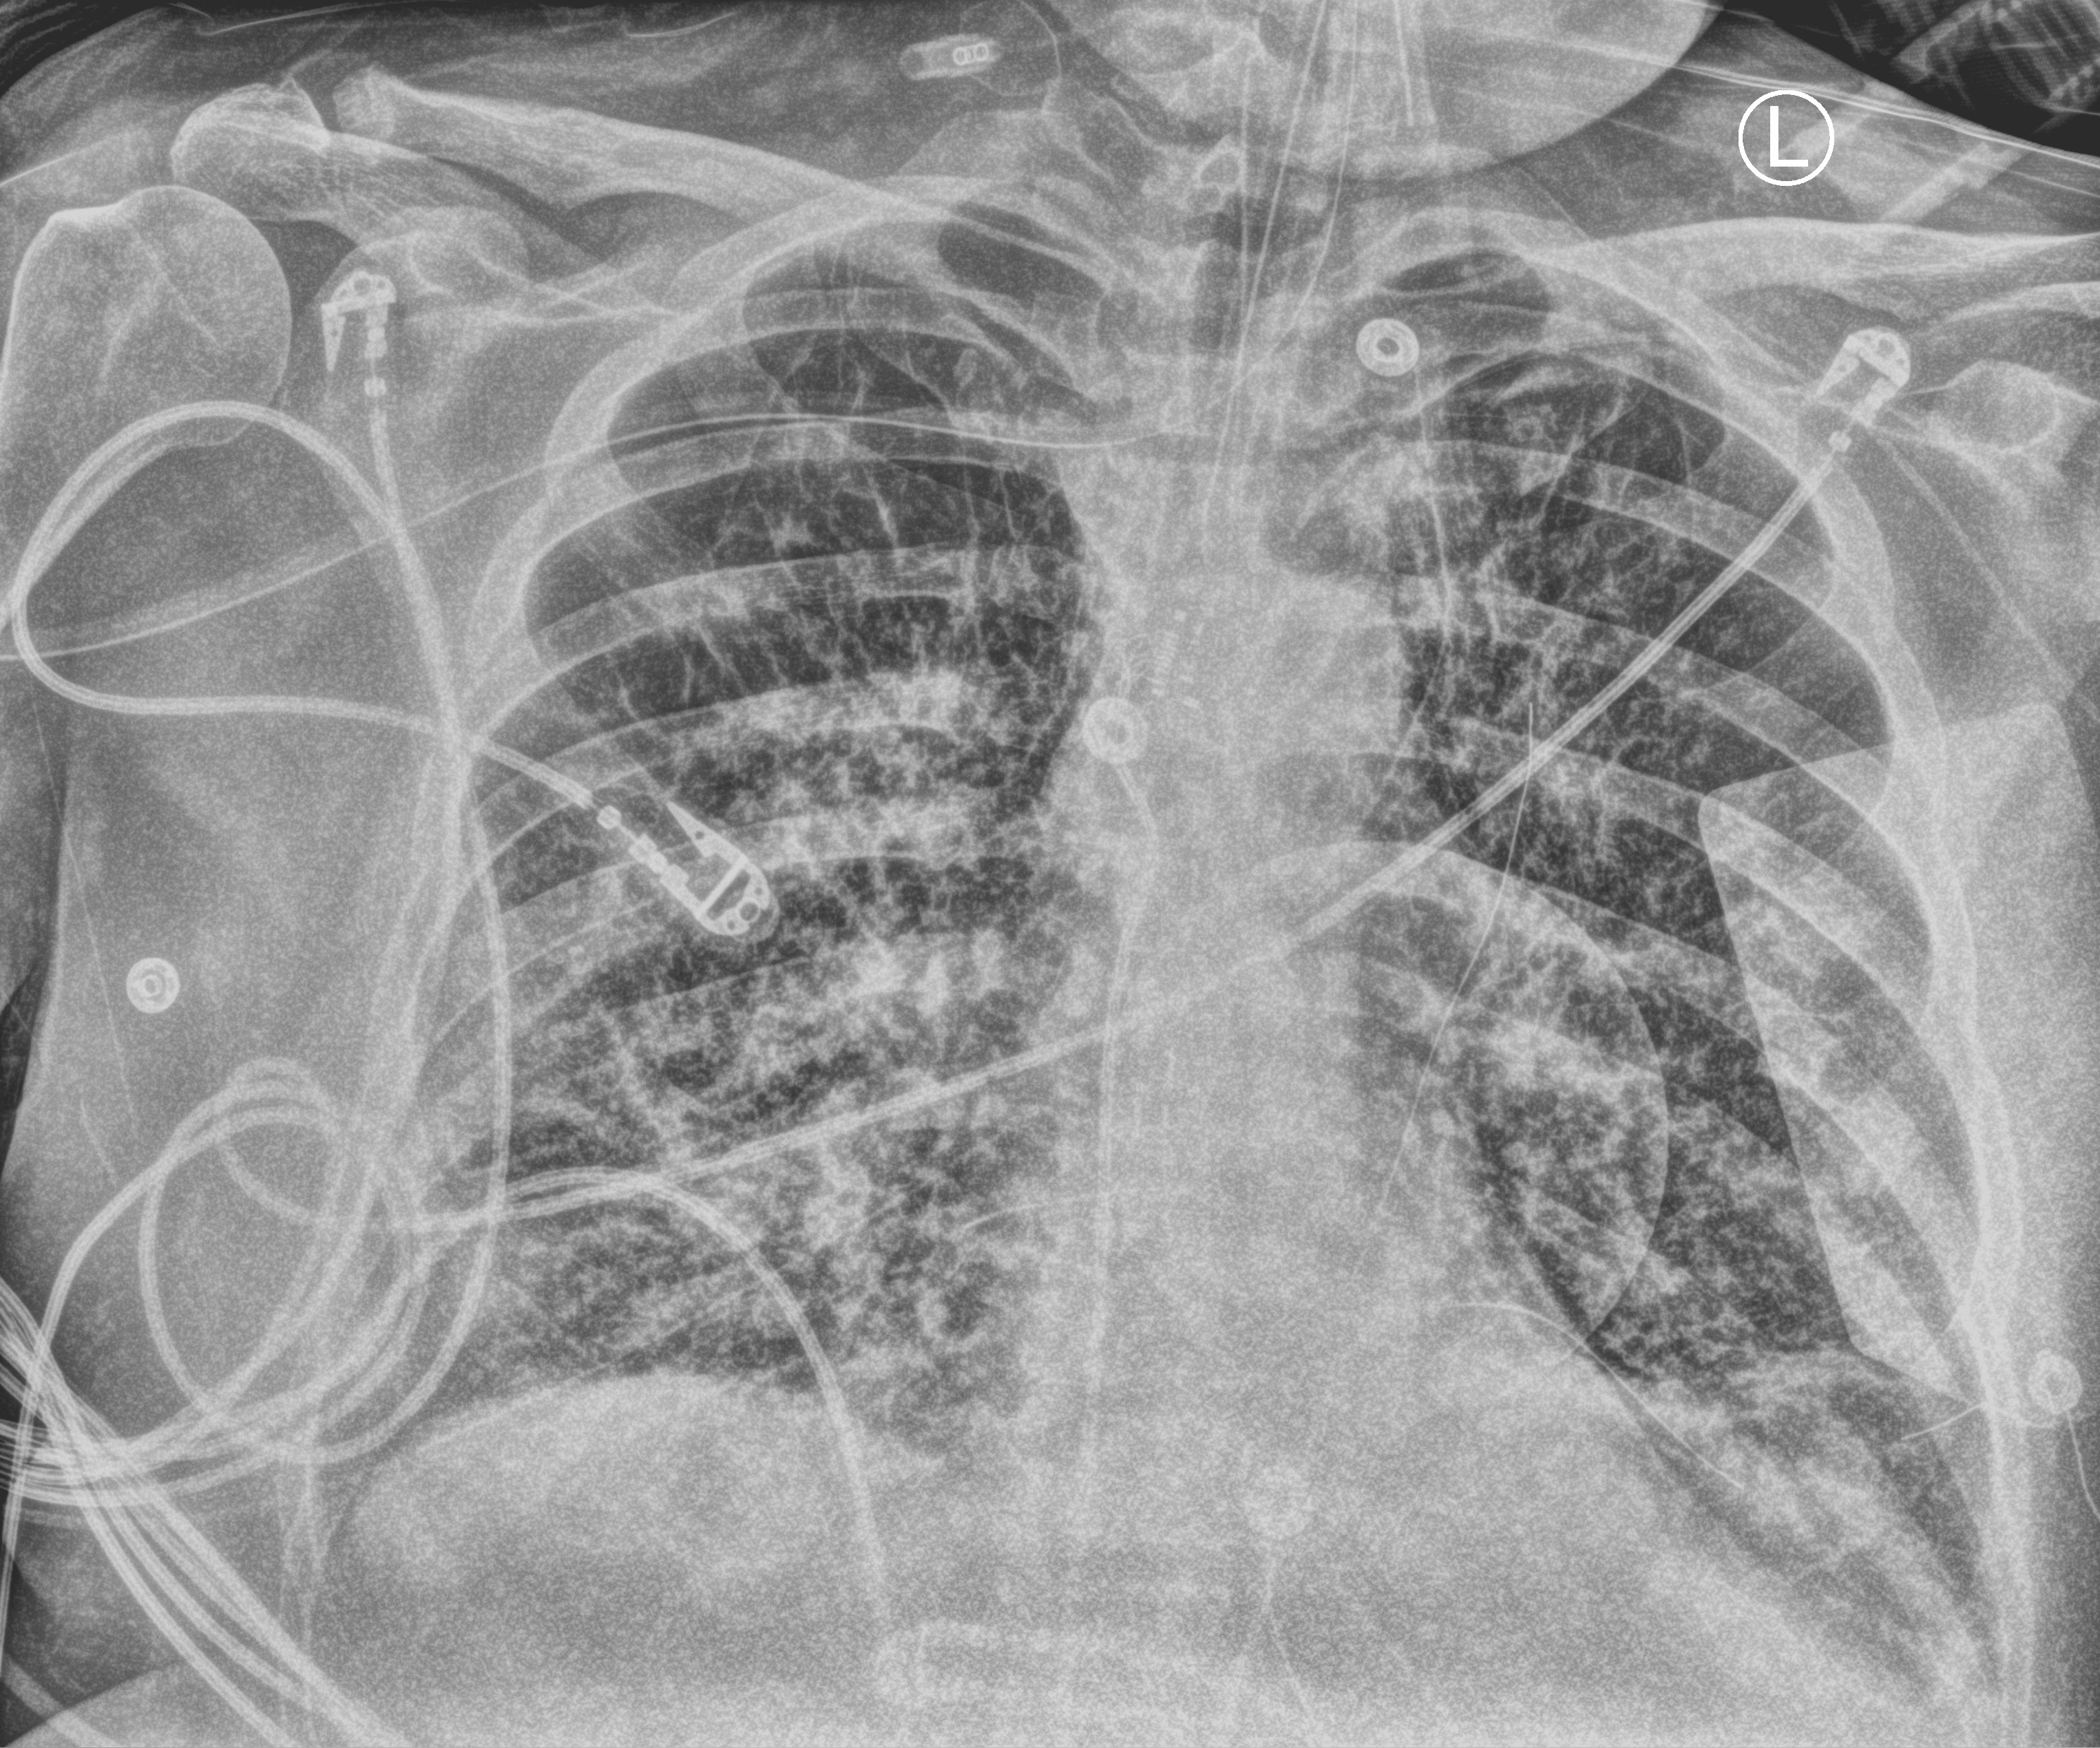
Chest X-ray (portable), anteroposterior (AP) projection. Adult patient hospitalised with COVID-19, age 18–59 years.
From the hospital-stay record, not from the radiograph (when in the stay this image was taken is not recorded):
- admitted to intensive care during this hospital stay: yes
- other chronic lung disease (admission record): yes
- COPD (admission record): yes